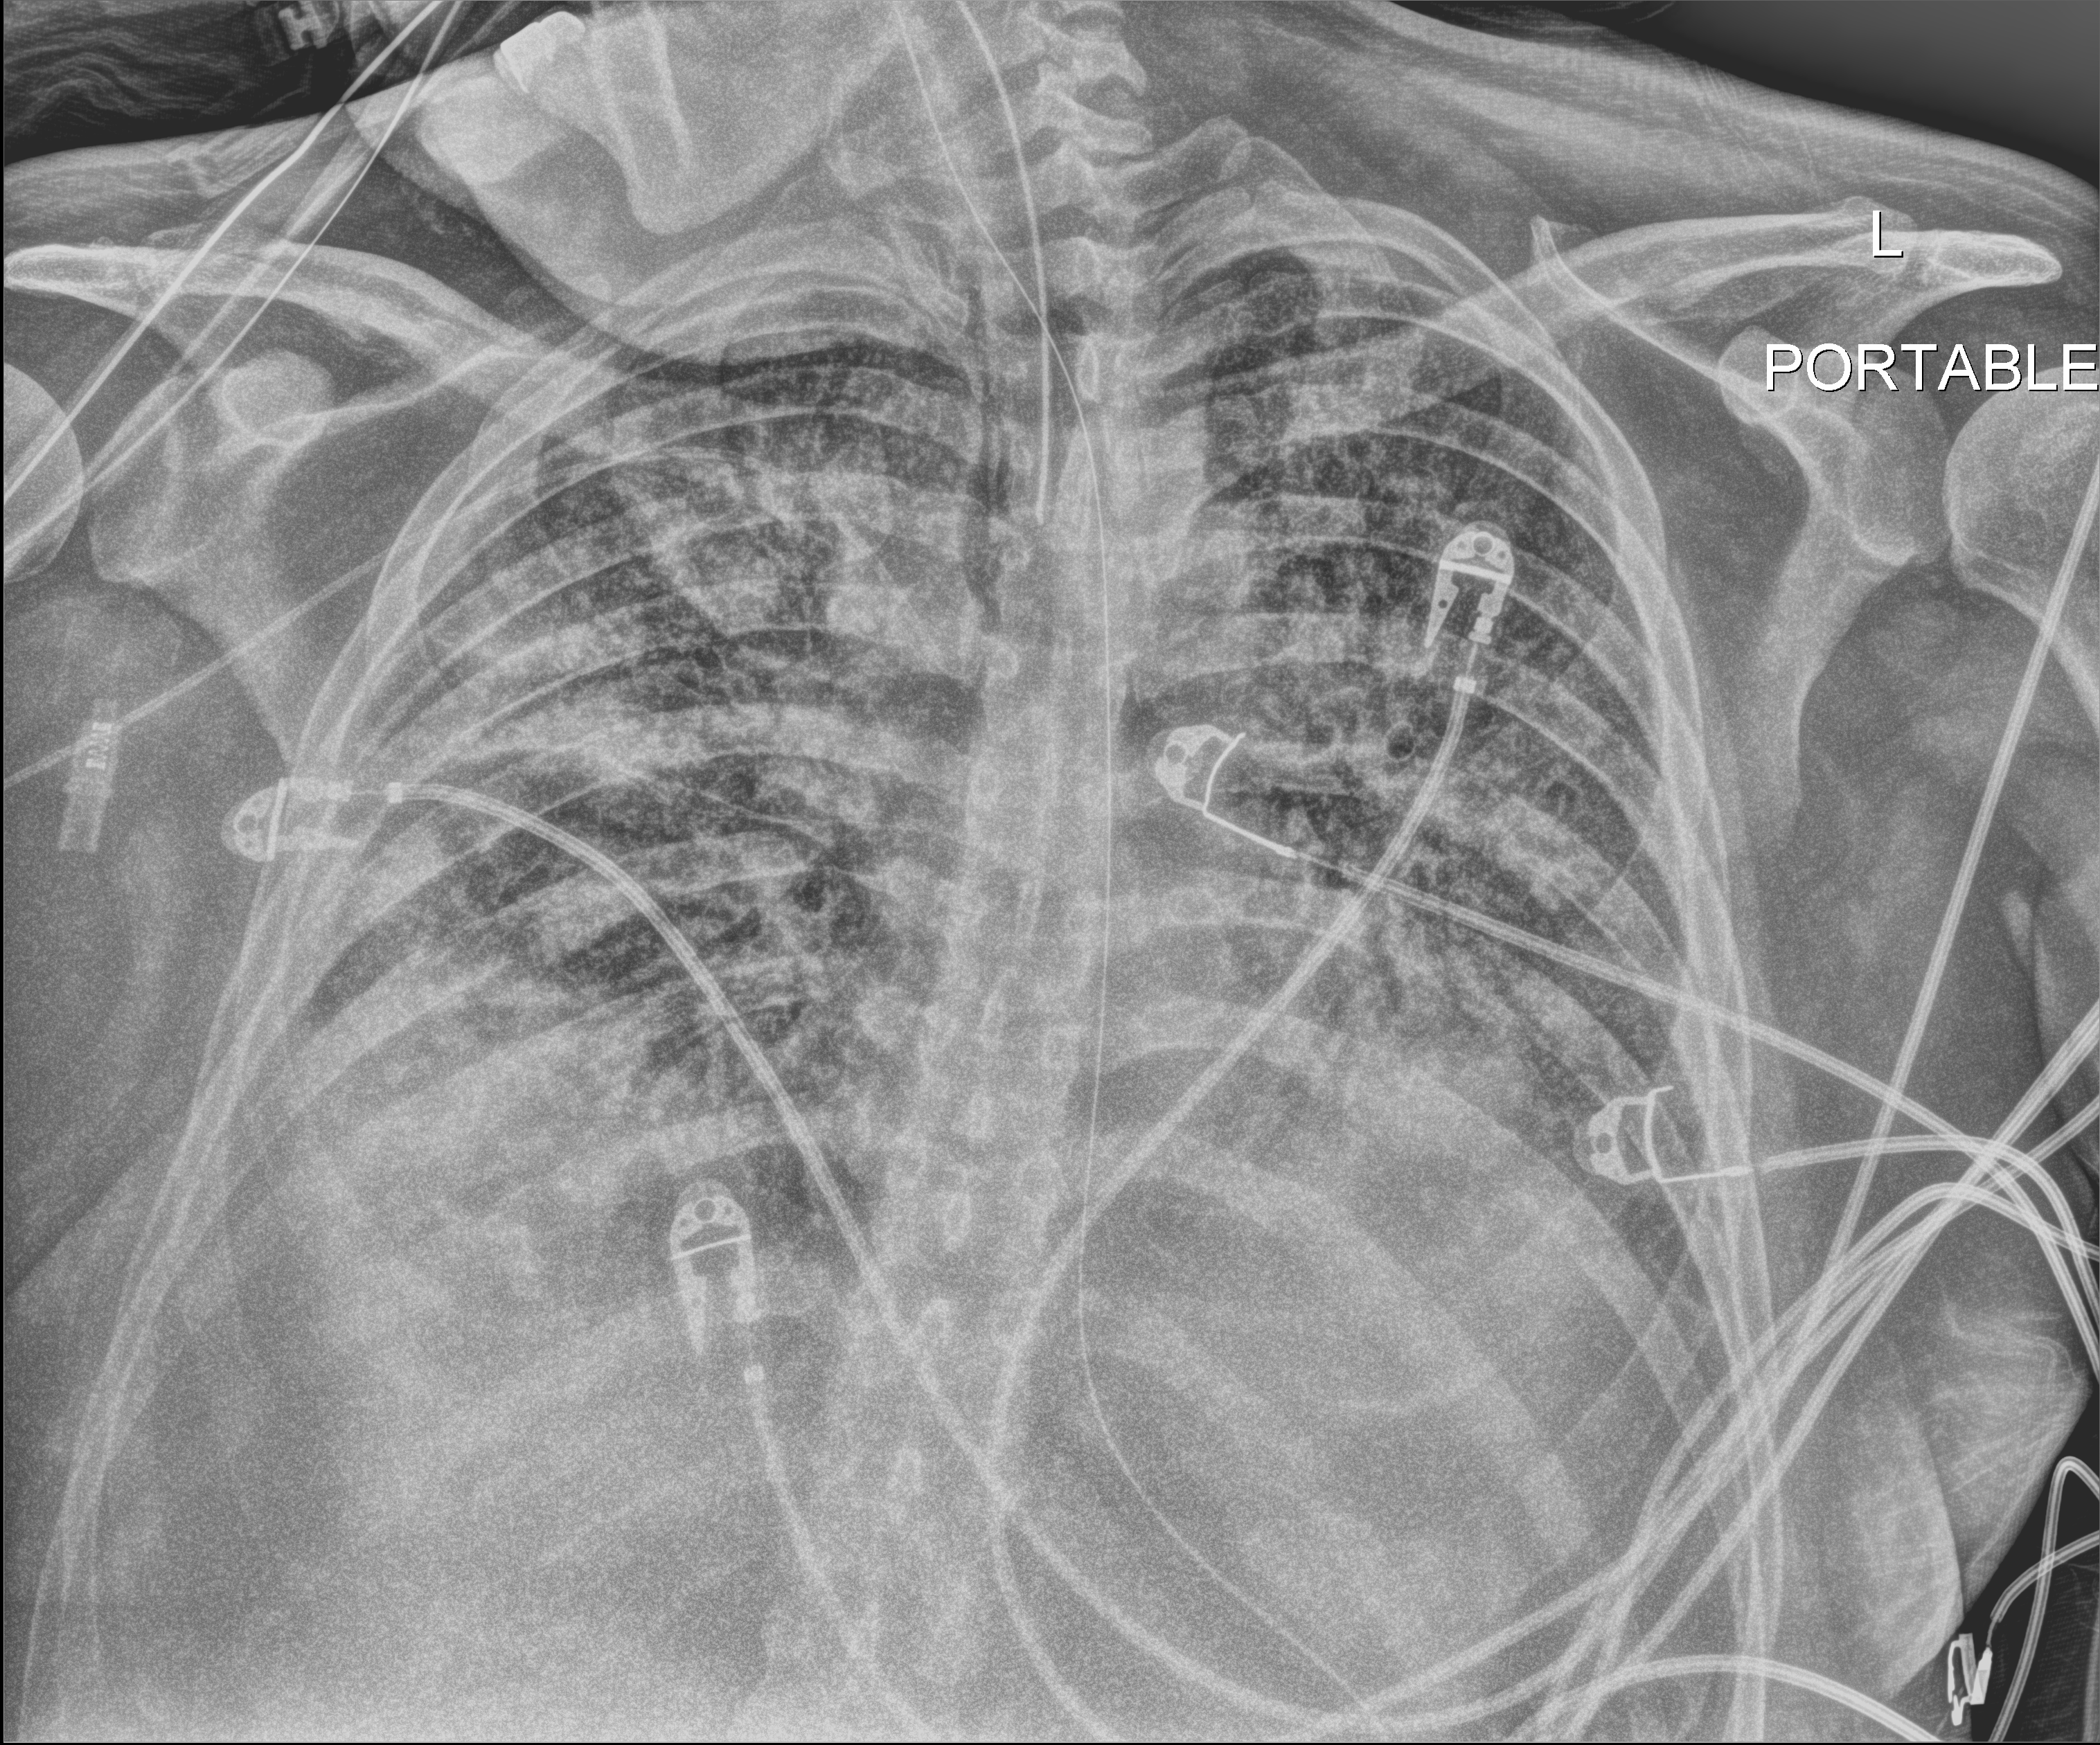
Chest X-ray (portable); anteroposterior (AP) projection. Male patient hospitalised with COVID-19, age 18–59 years.
Admission-level facts for this patient (not findings on this image; timing relative to this image not recorded): mechanically ventilated during this hospital stay: yes.